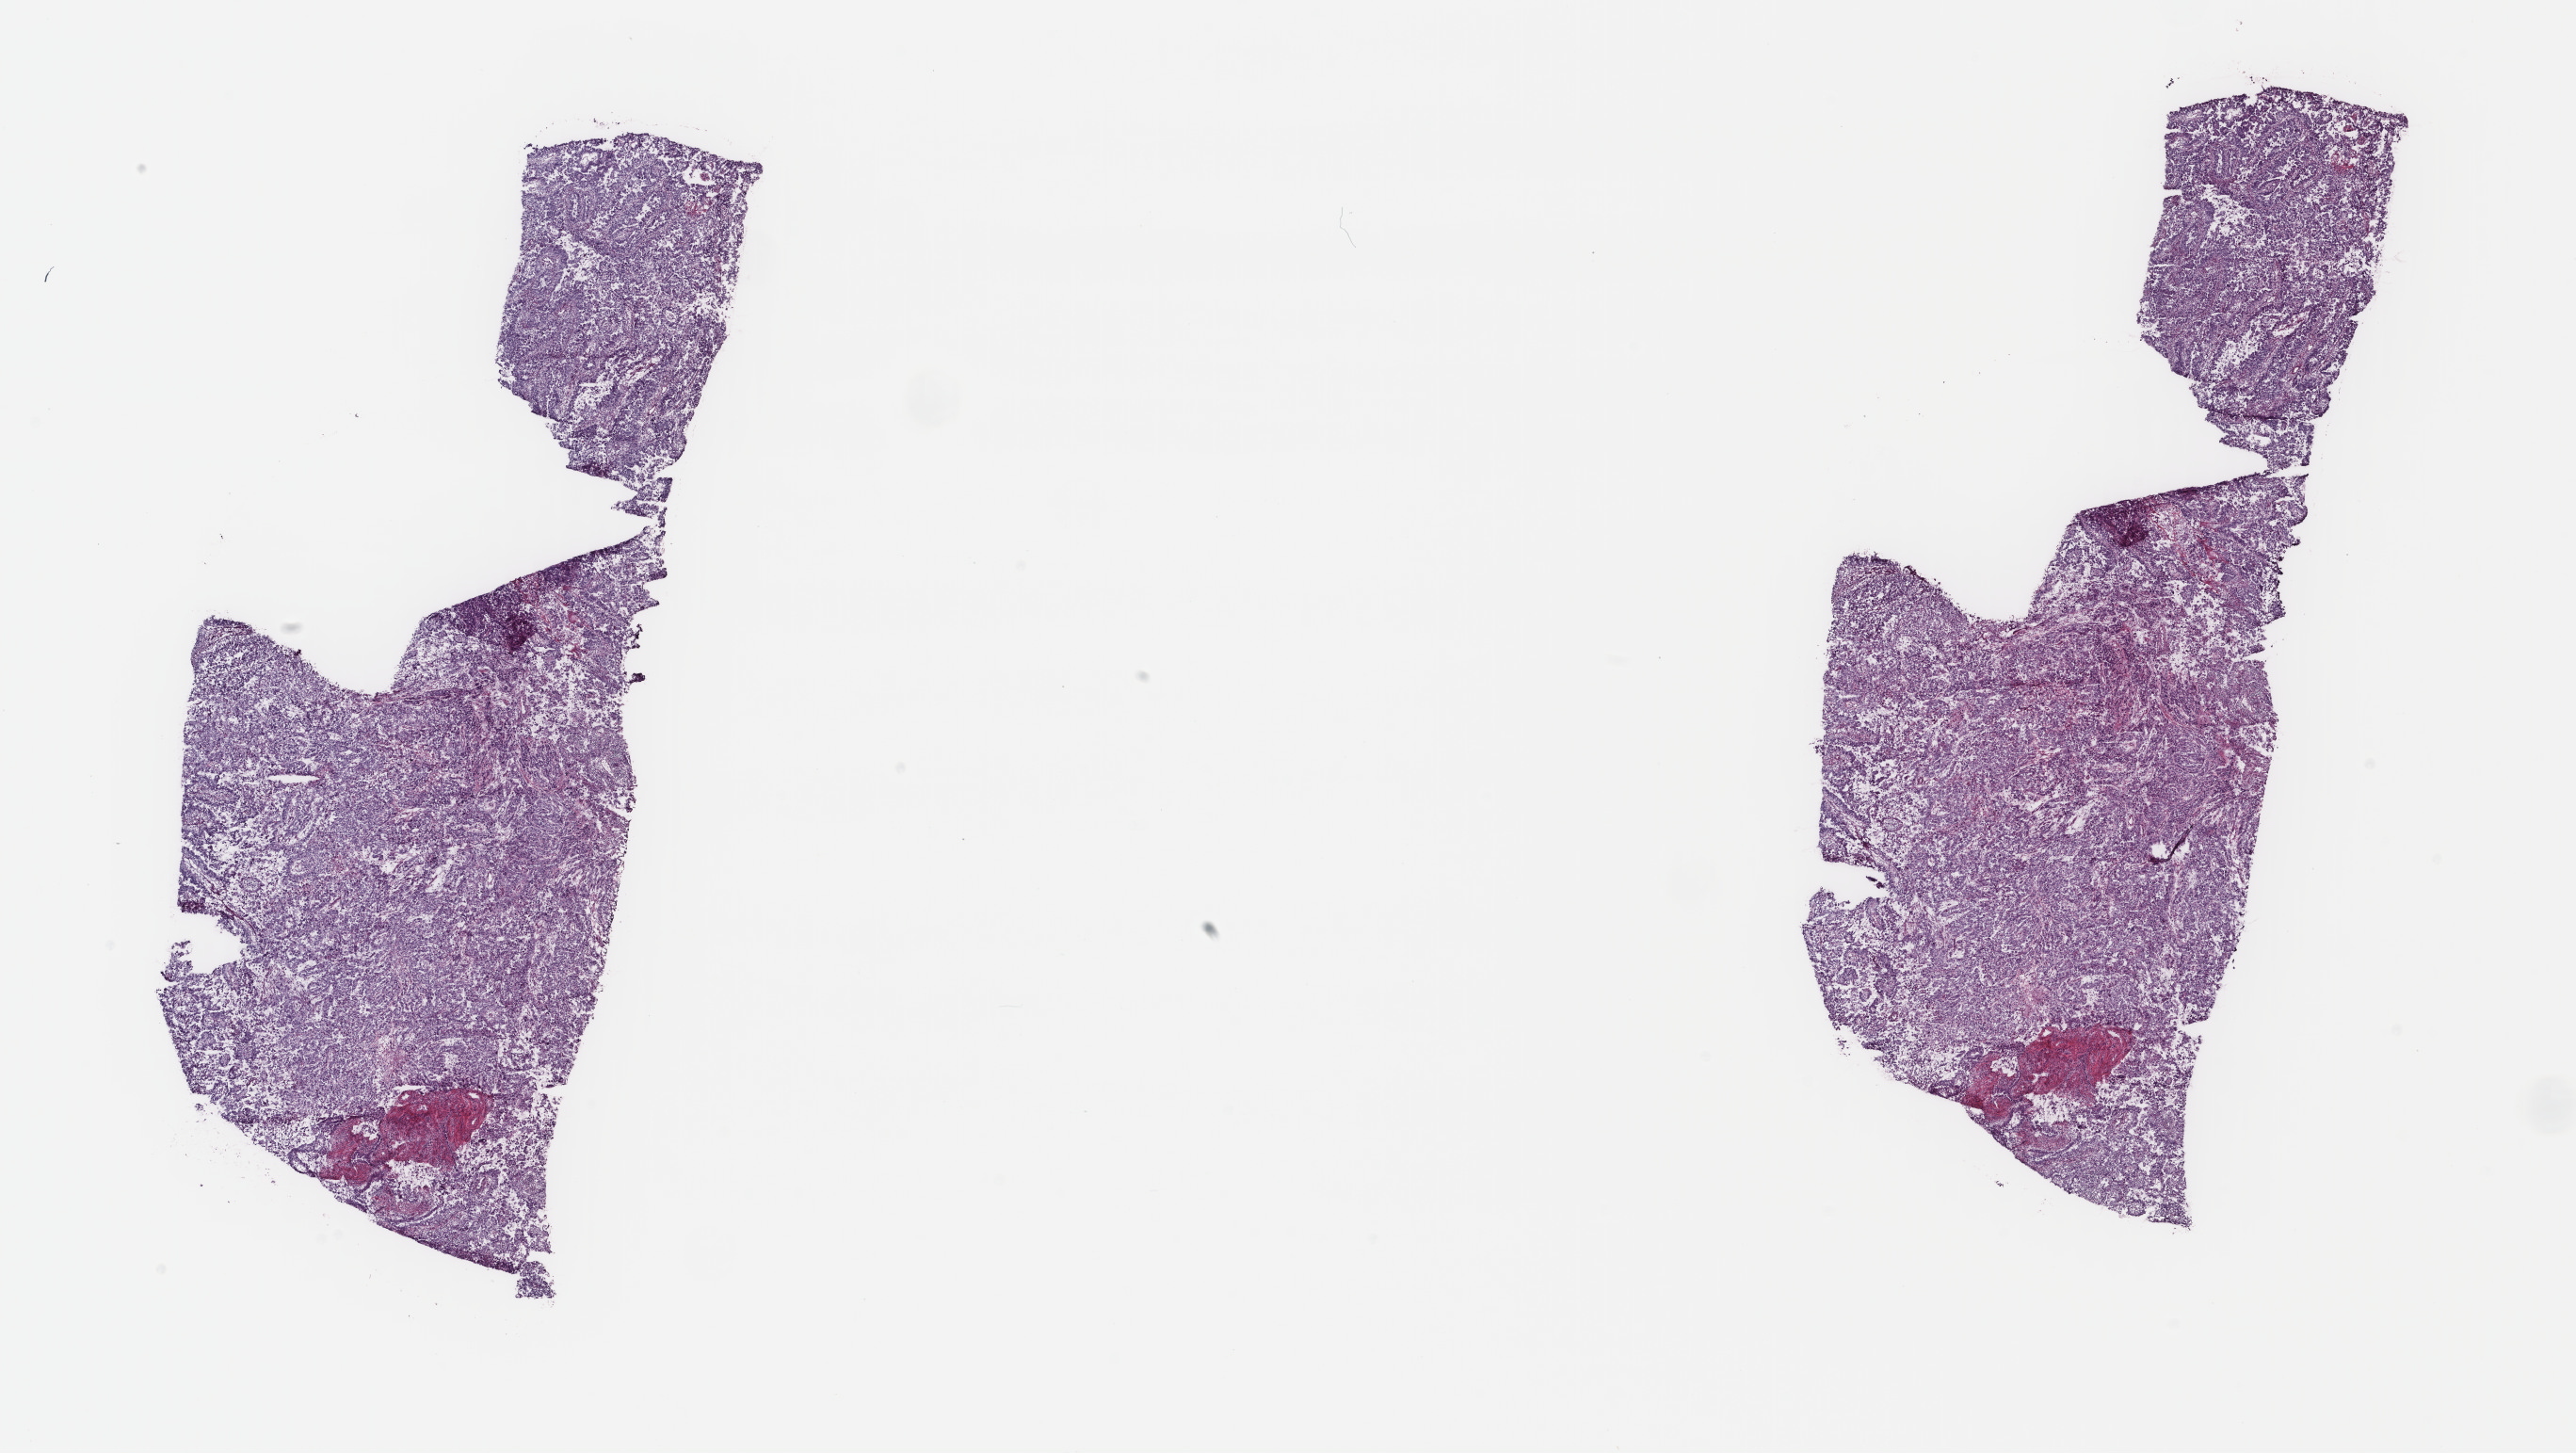
Digitized H&E tissue section (whole slide), shown as a low-resolution overview of the whole scanned area (about 21.7 x 12.2 mm), frozen section from the top of the tissue portion, sample: primary tumour, uterus. Patient: female, age at initial diagnosis 57 years. Histologic grade: G3 (poorly differentiated). Slide review estimates, as recorded: tumour cells 90%, tumour nuclei 95%, normal cells 5%, stromal cells 2%, necrosis 3%. Infiltration values recorded for this section: lymphocyte infiltration 2%, monocyte infiltration 0%, neutrophil infiltration 0%.
* histologic diagnosis: Papillary serous cystadenocarcinoma (endometrium)
* FIGO stage: IIIC2
* lymph nodes positive (case pathology): 3 of 17 examined